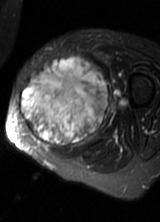
MRI of an extremity soft-tissue mass, one axial slice; slice 29 of 69 in the series (ordered by position); T2-weighted fat-saturated; MR volume resampled by the dataset authors to the PET/CT grid (not the native acquisition matrix); 3.27 mm slice thickness; 160 × 222 image matrix, field of view 156 × 217 mm. Female patient. Case-level facts recorded for this patient, not image findings: histological type: pleomorphic leiomyosarcoma; grade: high; site of the primary tumour: left thigh.
Annotated regions visible in this slice (expert contour drawn on MRI and transferred to this co-registered scan by the dataset authors):
- gross tumour volume including surrounding oedema: bounding box [x1, y1, x2, y2] px = [18, 59, 110, 149]
- gross tumour volume (mass): [18, 59, 108, 149]